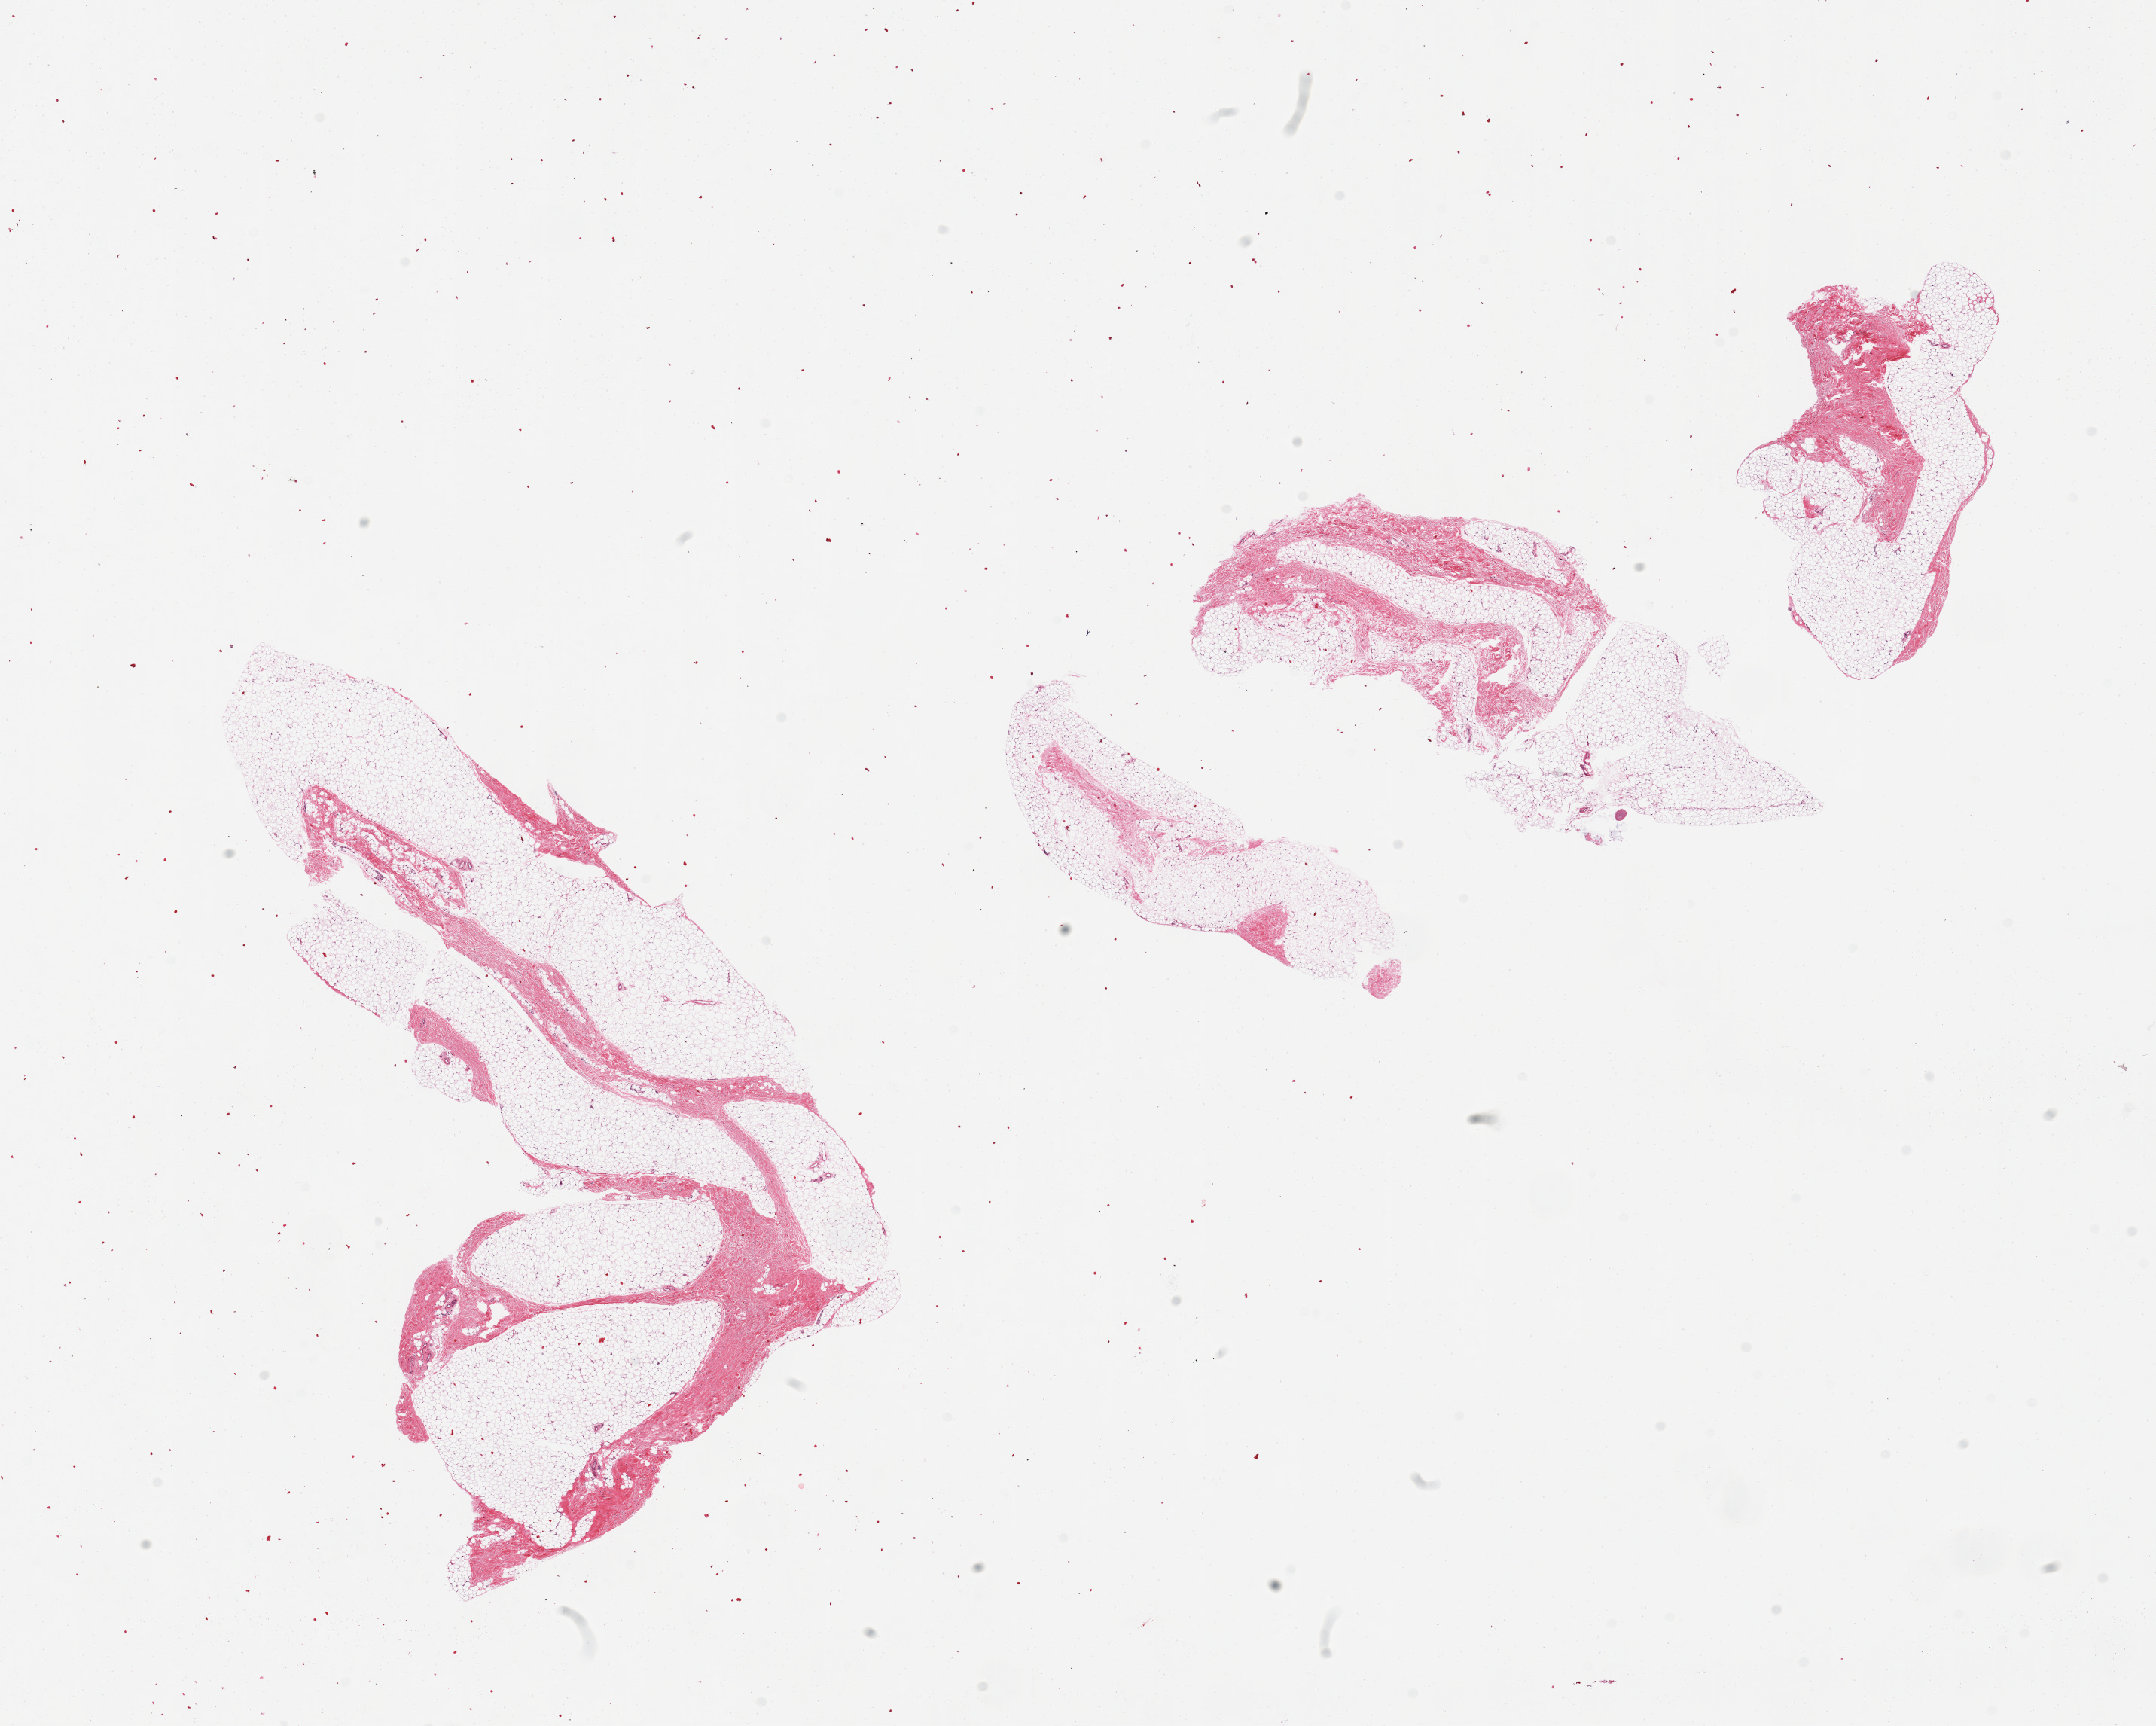
Hematoxylin and eosin (H&E) whole-slide image, brightfield — whole scanned area (about 22.6 x 18.1 mm, slide scanned at 20x) shown as a low-resolution overview, PAXgene-fixed paraffin-embedded (PFPE) section, section of breast (target tissue), donor tissue sample. Donor sex: male.
• review note (as recorded): 4 pieces, predominantly fat with ~10-20% fibrous stroma, no ducts